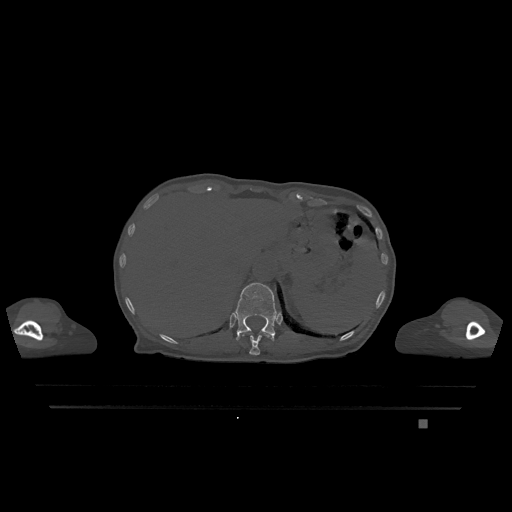
CT including the spine, one axial slice; position 551 of 1317 along the scan axis; bone window (W 1800 / L 400 HU); 0.5 mm slice thickness; 512 × 512 image matrix, field of view 500 × 500 mm. Female patient, age 74 years. Case-level facts recorded for this patient, not image findings: primary cancer: lung; vertebrae with lytic lesions (as recorded): T1, T4, T5, T6, L4, L5.
Annotated regions visible in this slice (semi-automatically segmented with operator editing):
- T11 vertebra: bounding box (x1, y1, x2, y2) in pixels: (242, 332, 272, 355)
- T12 vertebra: (235, 282, 278, 341)